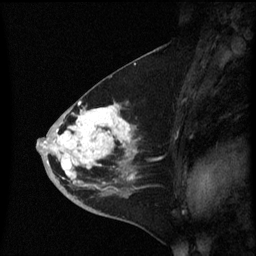
Breast MRI (dynamic contrast-enhanced), one sagittal slice; slice 30 of 60 in the series (ordered by position); dynamic contrast-enhanced series, image 2 of 3 at this slice position (ordered by acquisition); 1.5 T; TE 4.2 ms, TR 8.4 ms; 2.3 mm slice thickness; 256 × 256 image matrix, field of view 200 × 200 mm. Female patient, age 46 years. From the clinical record (not read from this slice): setting: breast cancer imaged before/during neoadjuvant chemotherapy; receptor status: HER2-positive.
Structures marked on this image (semi-automatic segmentation, software-assisted and operator-edited):
- analysis volume of interest (the breast-tissue region the enhancement analysis was run in; not a lesion): bounding box [x1, y1, x2, y2] px = [37, 96, 141, 187]
- tumour enhancement mask (voxels above the 70 % enhancement threshold inside the analysis volume of interest): [44, 102, 136, 181]